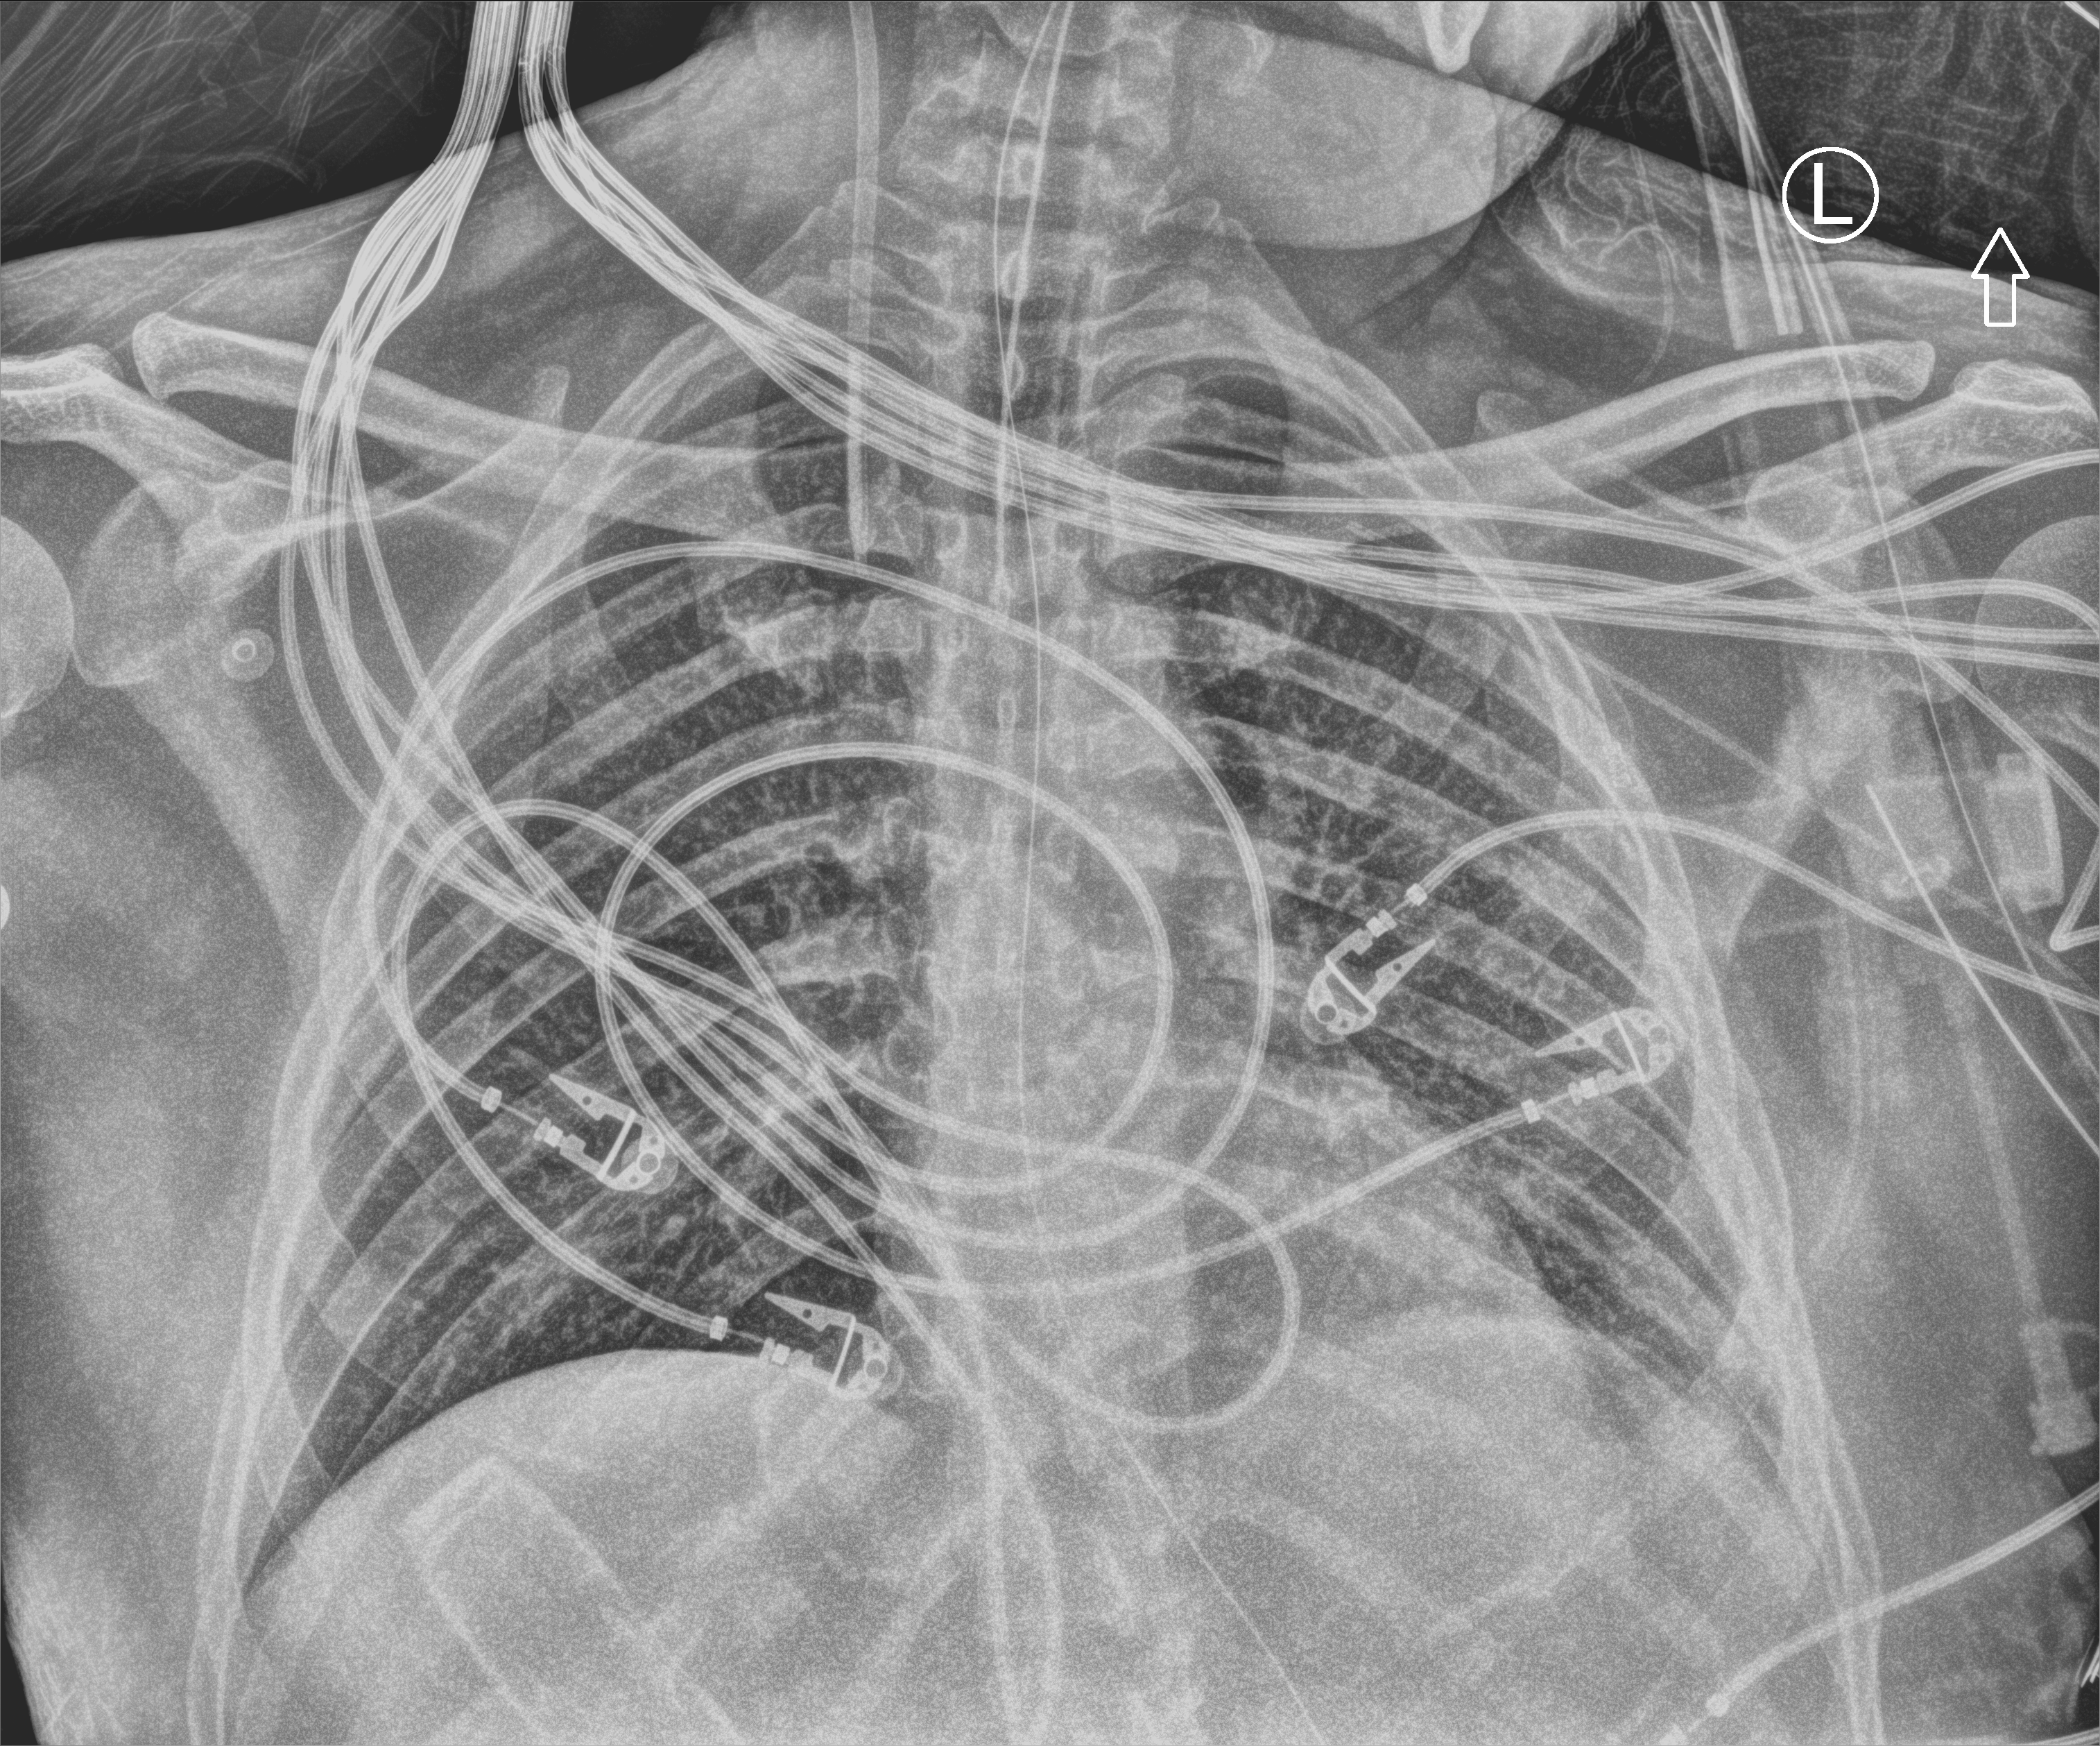
Portable chest radiograph, anteroposterior (AP) projection. Patient hospitalised with COVID-19, aged 18–59 years.
From the hospital-stay record, not from the radiograph (when in the stay this image was taken is not recorded): admitted to intensive care during this hospital stay: yes.